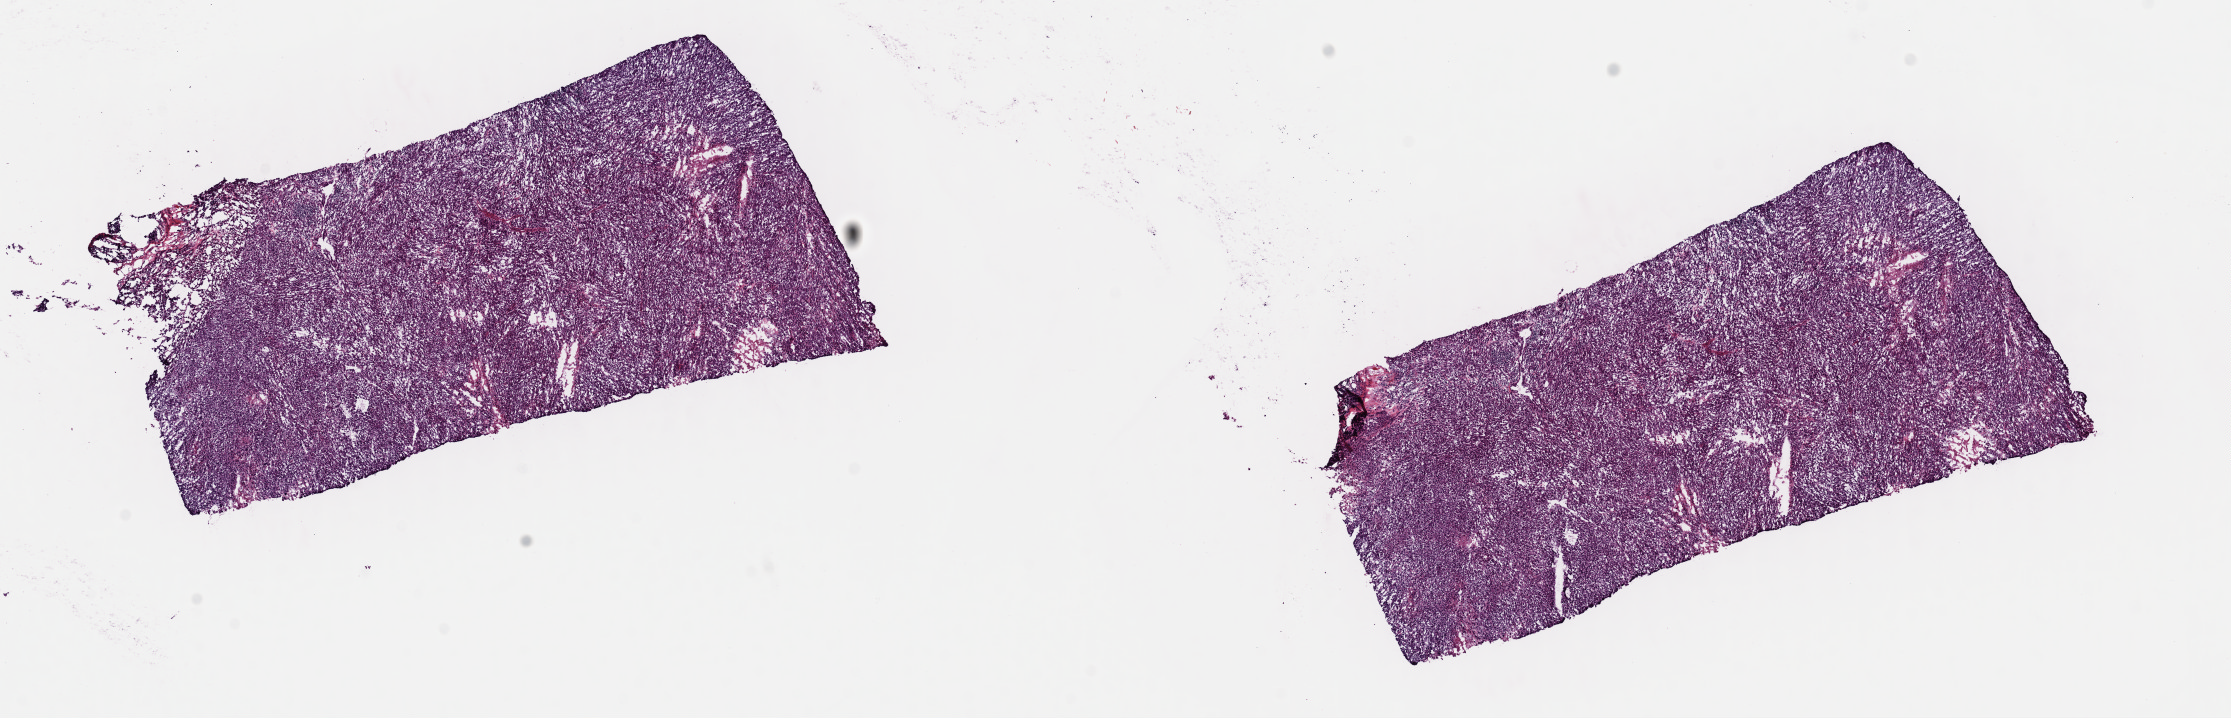
Whole-slide histology image, H&E-stained — a low-resolution overview of the entire scanned area, about 17.6 x 5.7 mm (from a 40x scan), frozen section from the top of the tissue portion, metastatic tumour sample, sampled site not recorded. Male, age 78 years at initial diagnosis. Composition of this section per pathologist review: tumour cells 90%, tumour nuclei 90%, normal cells 0%, stromal cells 10%, necrosis 0%. Infiltration values recorded for this section: lymphocyte infiltration 2%, monocyte infiltration 1%, neutrophil infiltration 0%.
* this section: metastatic tumour tissue
* patient diagnosis: Malignant melanoma, NOS